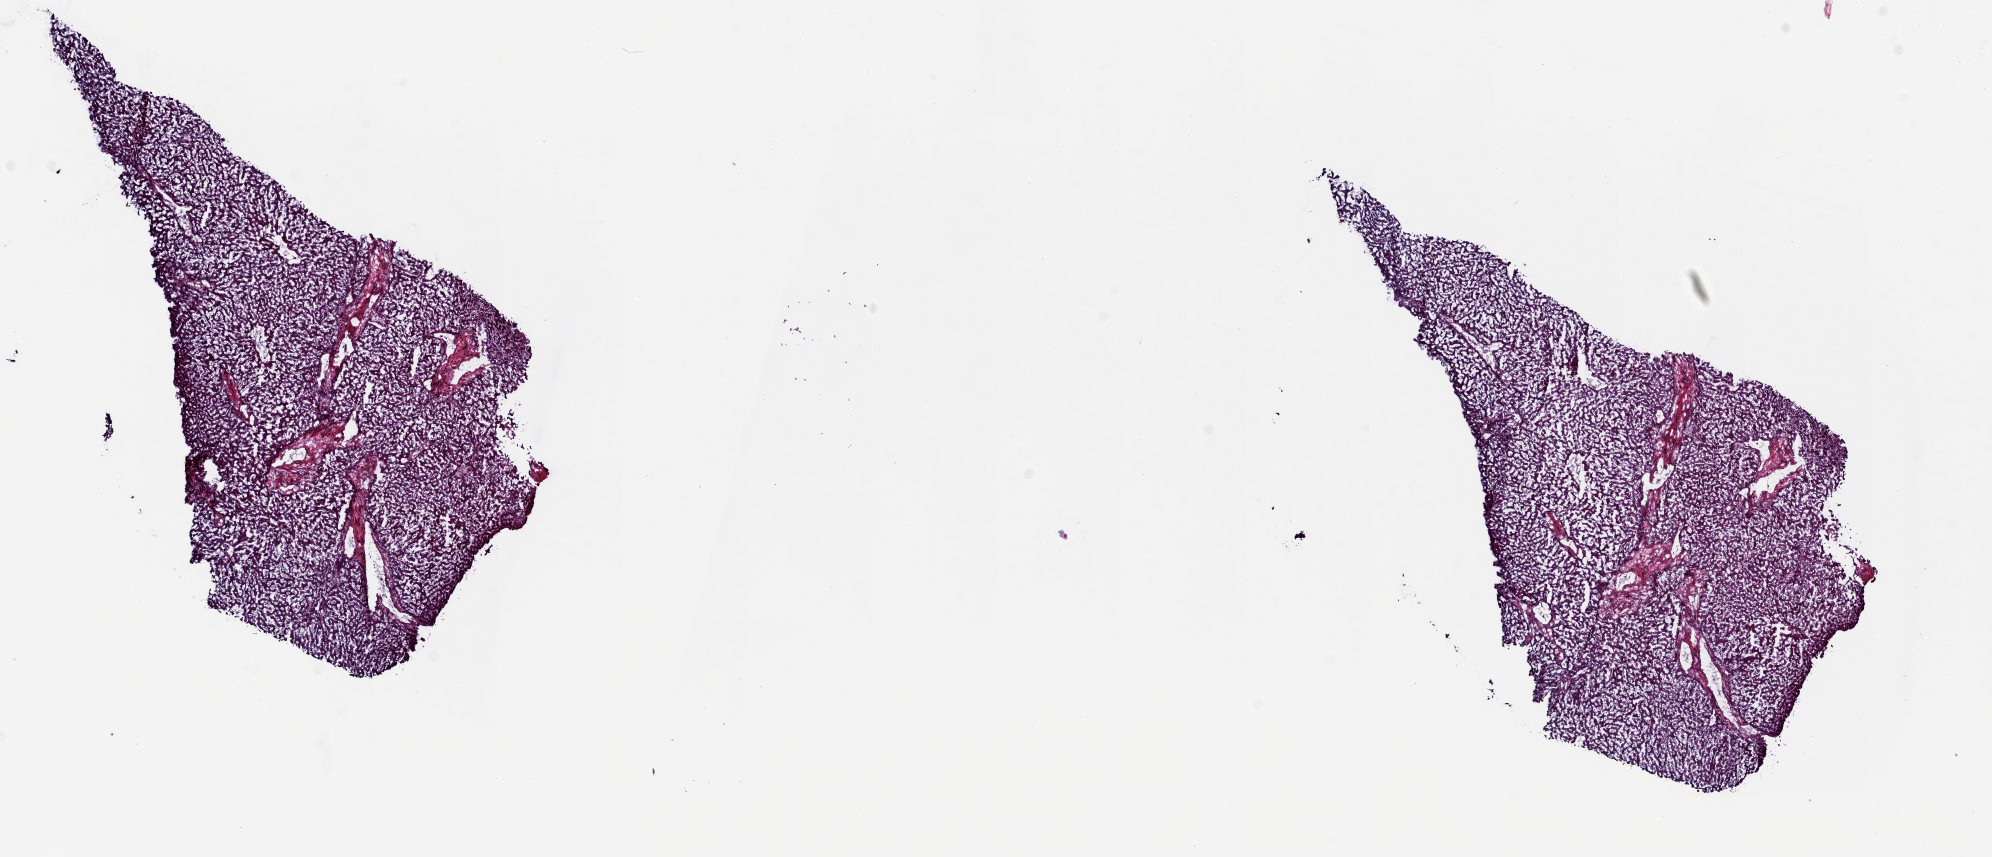
Whole-slide histology image, H&E-stained, whole scanned area (about 15.8 x 6.8 mm, slide scanned at 20x) shown as a low-resolution overview; frozen section from the top of the tissue portion; sample: solid tissue normal (non-tumour tissue), liver. Patient: male, age at initial diagnosis 67 years. Composition of this section per pathologist review: tumour cells 0%, tumour nuclei 0%, normal cells 70%, stromal cells 30%, necrosis 0%. Inflammatory infiltration, as recorded: lymphocyte infiltration 5%, monocyte infiltration 0%, neutrophil infiltration 0%.
* this section: solid tissue normal sample (biorepository sample class)
* patient diagnosis: Hepatocellular carcinoma, NOS